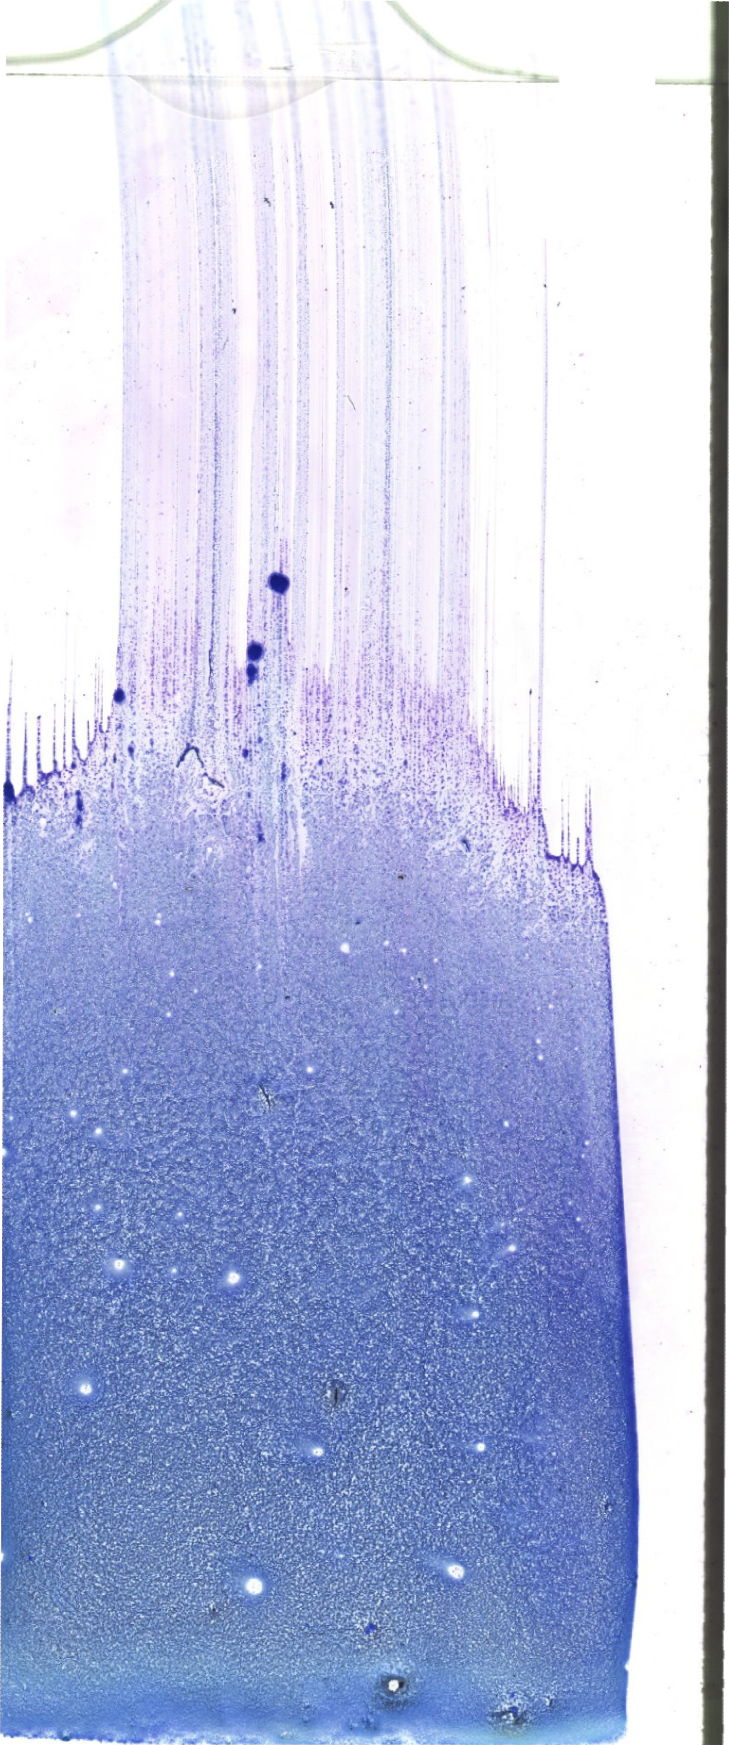
Whole-slide image of a May-Grünwald–Giemsa-stained bone marrow aspirate smear — low-resolution overview of the scanned area, about 20.7 x 49.5 mm. Female patient.
Diagnosis: Acute Myelomonocytic Leukemia.